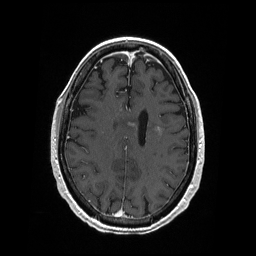
Brain MRI from a brain-tumour surgery series, one axial slice; slice 76 of 208 in the series (ordered by position); T1-weighted post-contrast; 256 × 256 image matrix, field of view 256 × 256 mm. Case-level facts recorded for this patient, not image findings: histopathology: Primary diffuse large B-cell lymphoma; tumour location: Left Corpus Callosum (Frontal).
Annotated regions visible in this slice (manually delineated by an expert):
- tumour: box from (x=127, y=121) to (x=164, y=132) px